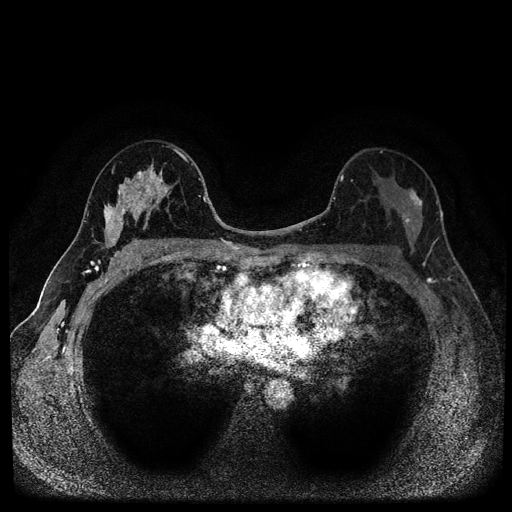
Breast MRI (dynamic contrast-enhanced, multi-phase), one axial slice. Slice 61 of 116 in the series (ordered by position). Dynamic contrast-enhanced series, time point 2 of 5 at this slice position (early post-contrast). 1.5 T. TE 2.7 ms, TR 5.4 ms. 2 mm slice thickness. 512 × 512 image matrix, field of view 320 × 320 mm. Female patient, age 49 years.
Outlined on this slice (semi-automatic segmentation, software-assisted and operator-edited):
- breast lesion (labelled benign in the annotation): bounding box [x1, y1, x2, y2] px = [100, 166, 172, 254]